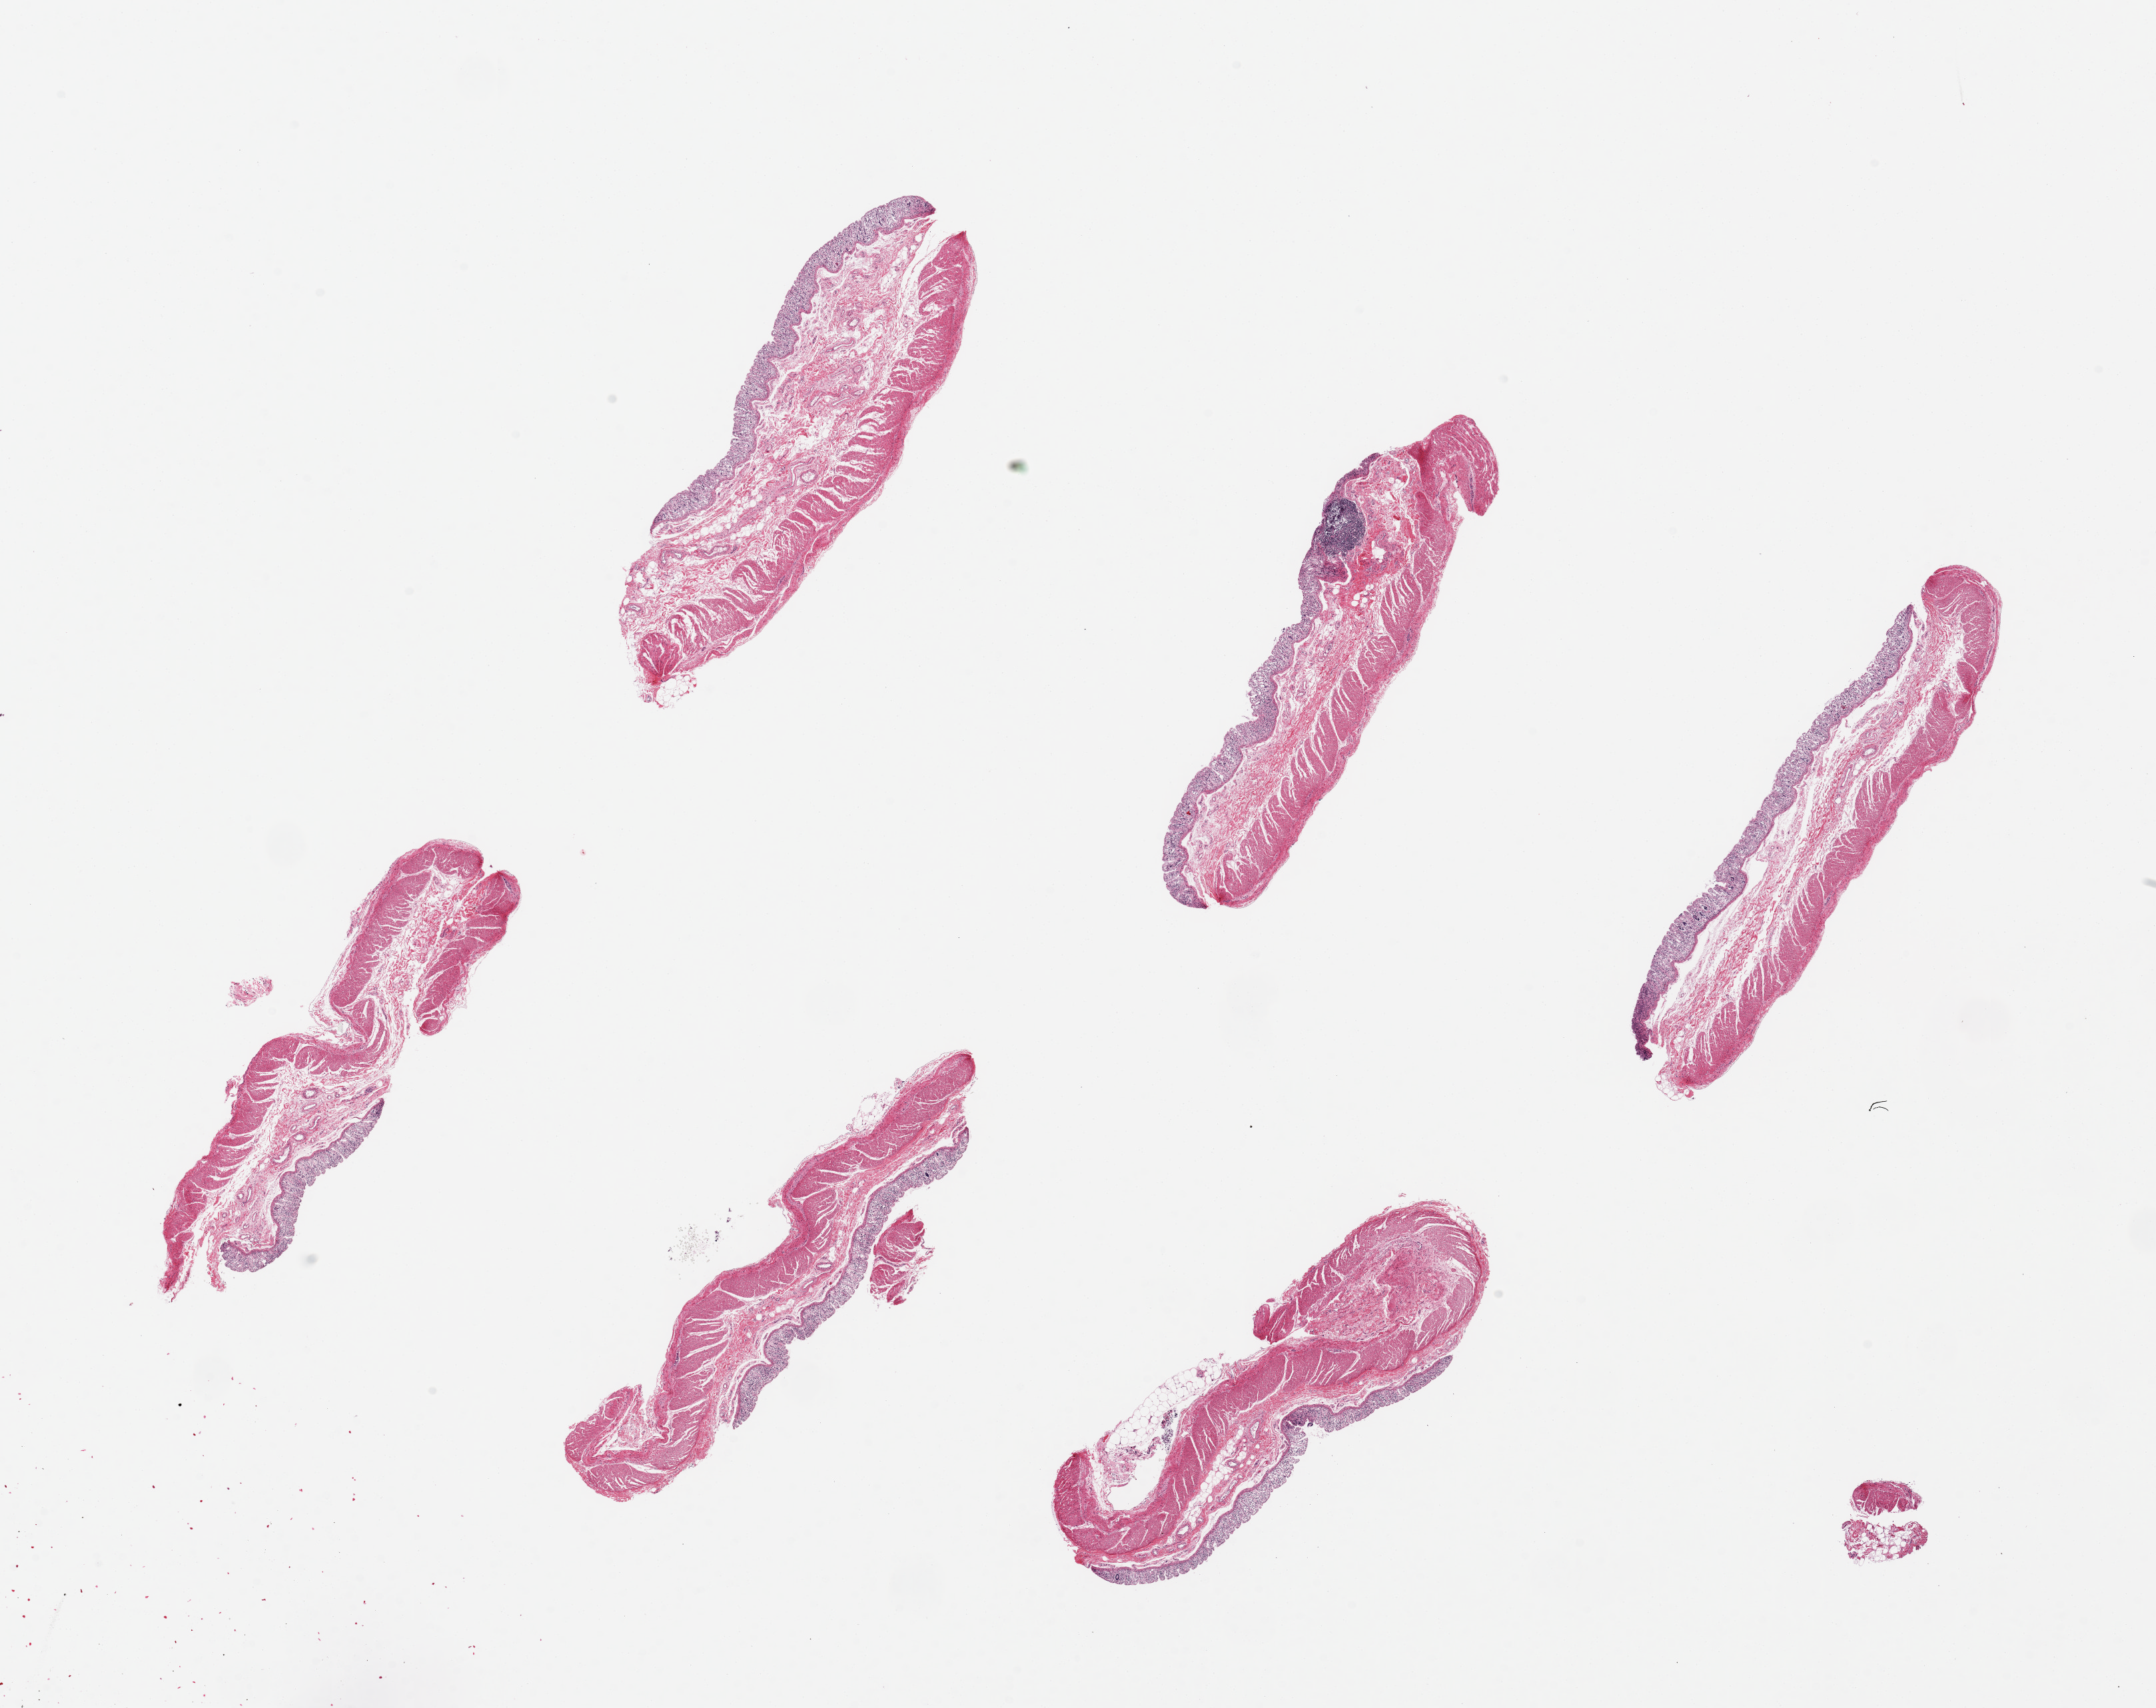
Whole-slide image, H&E stain, shown as a low-resolution overview of the whole scanned area (about 25.6 x 20.3 mm, slide scanned at 20x). PAXgene-fixed paraffin-embedded (PFPE) section. Sampled site (target tissue): transverse colon. Donor tissue sample. Male donor.
• reviewer comment on this tissue sample: 6 pieces, up to 7x2mm; mucosa severely autolyzed, muscle mild autolysis